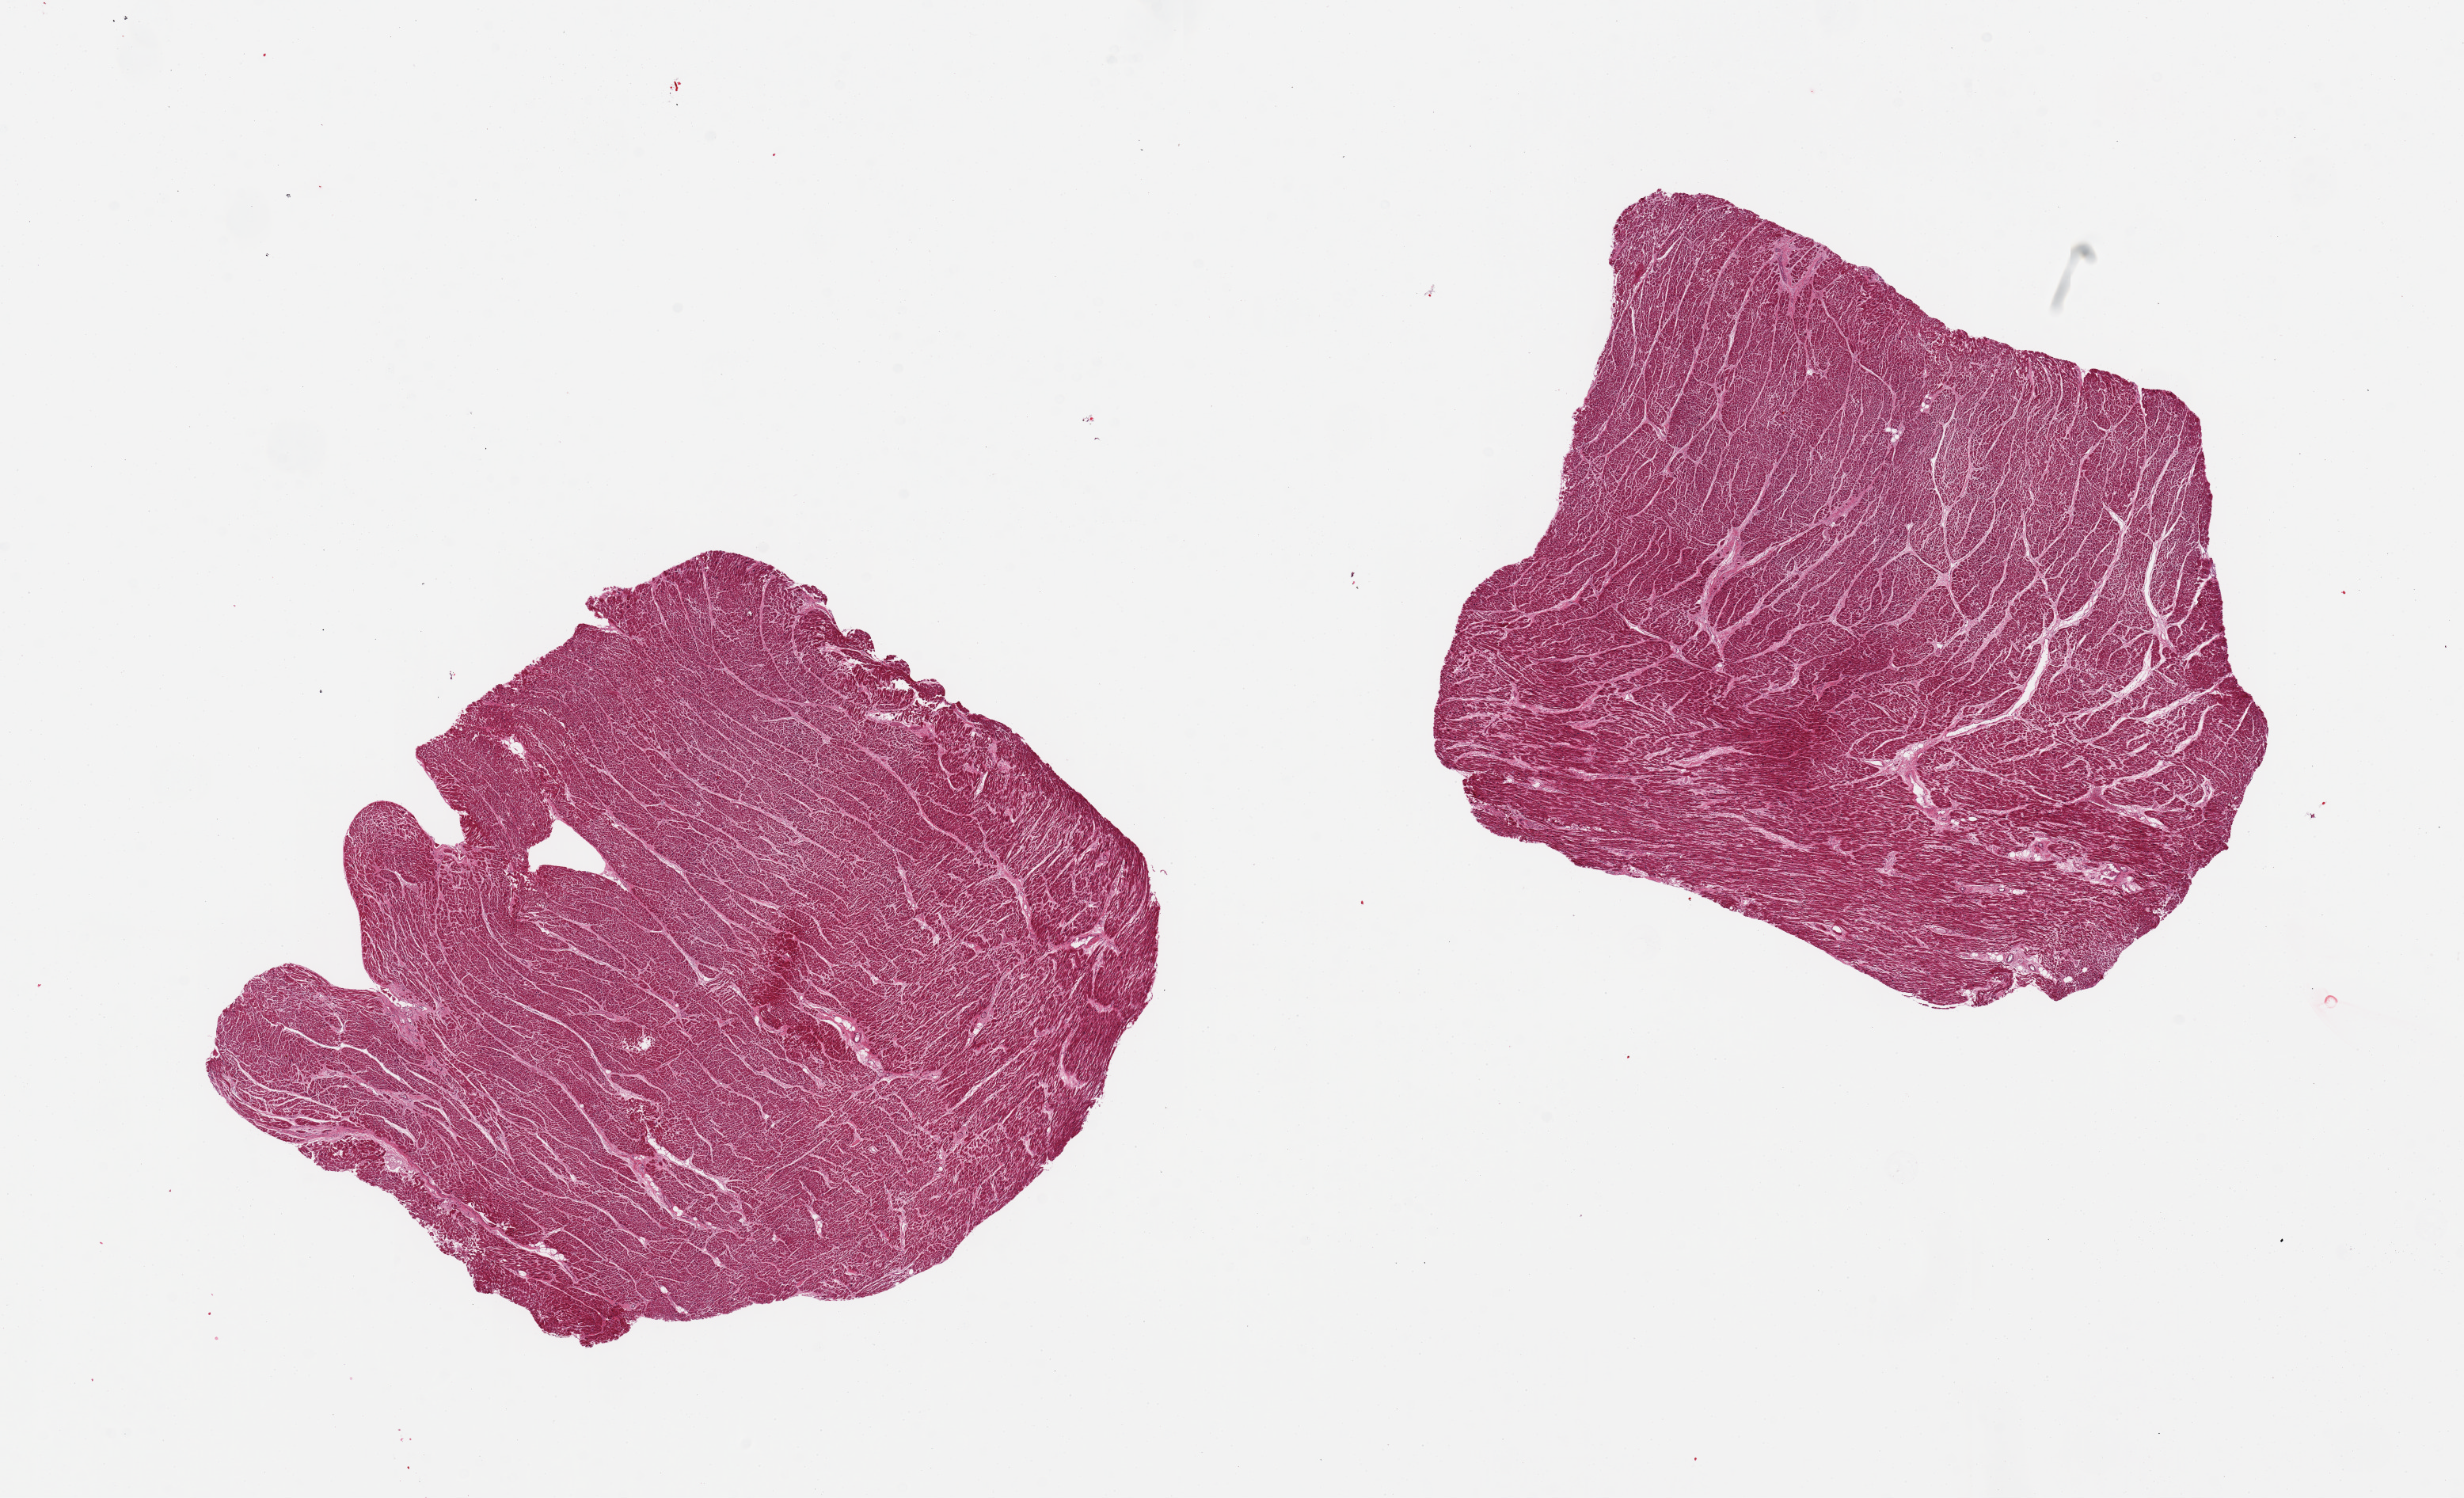
Haematoxylin and eosin whole-slide image, whole scanned area (about 24.6 x 15.0 mm, slide scanned at 20x) shown as a low-resolution overview; PAXgene-fixed paraffin-embedded (PFPE) section; sampled site (target tissue): heart; tissue donor sample.
Pathologist's review note for this sample: 2 pieces; hypertrophied fibers.